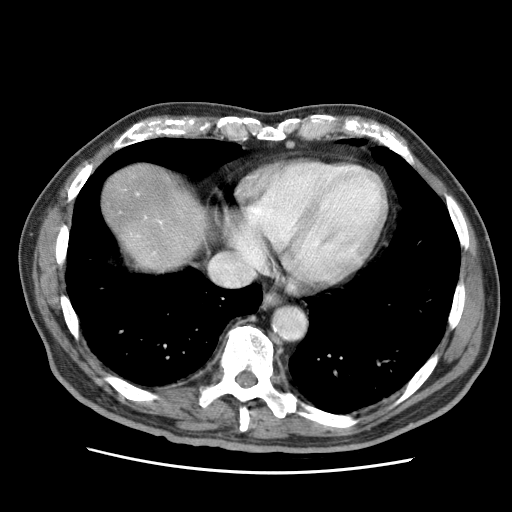
Contrast-enhanced abdominal CT (liver protocol), one axial slice. Slice 63 of 75 in the series (ordered by position). 120 kVp. Soft-tissue window (W 400 / L 40 HU). 2.5 mm slice thickness. 512 × 512 image matrix, field of view 360 × 360 mm. From the clinical record (not read from this slice): diagnosis: hepatocellular carcinoma (patient treated with transarterial chemoembolisation; whether this scan precedes or follows treatment is not stated here); TNM stage (as recorded): Stage-IIIA; Child-Pugh class: A; tumour differentiation: well differentiated; tumour nodularity: multinodular.
Annotated regions visible in this slice (semi-automatically segmented with operator editing):
- liver parenchyma outside the tumour (the mass and vessels are separate outlines, so this box may not span the whole liver): box from (x=102, y=164) to (x=206, y=270) px
- liver vessels: (x=136, y=217)–(x=162, y=255)